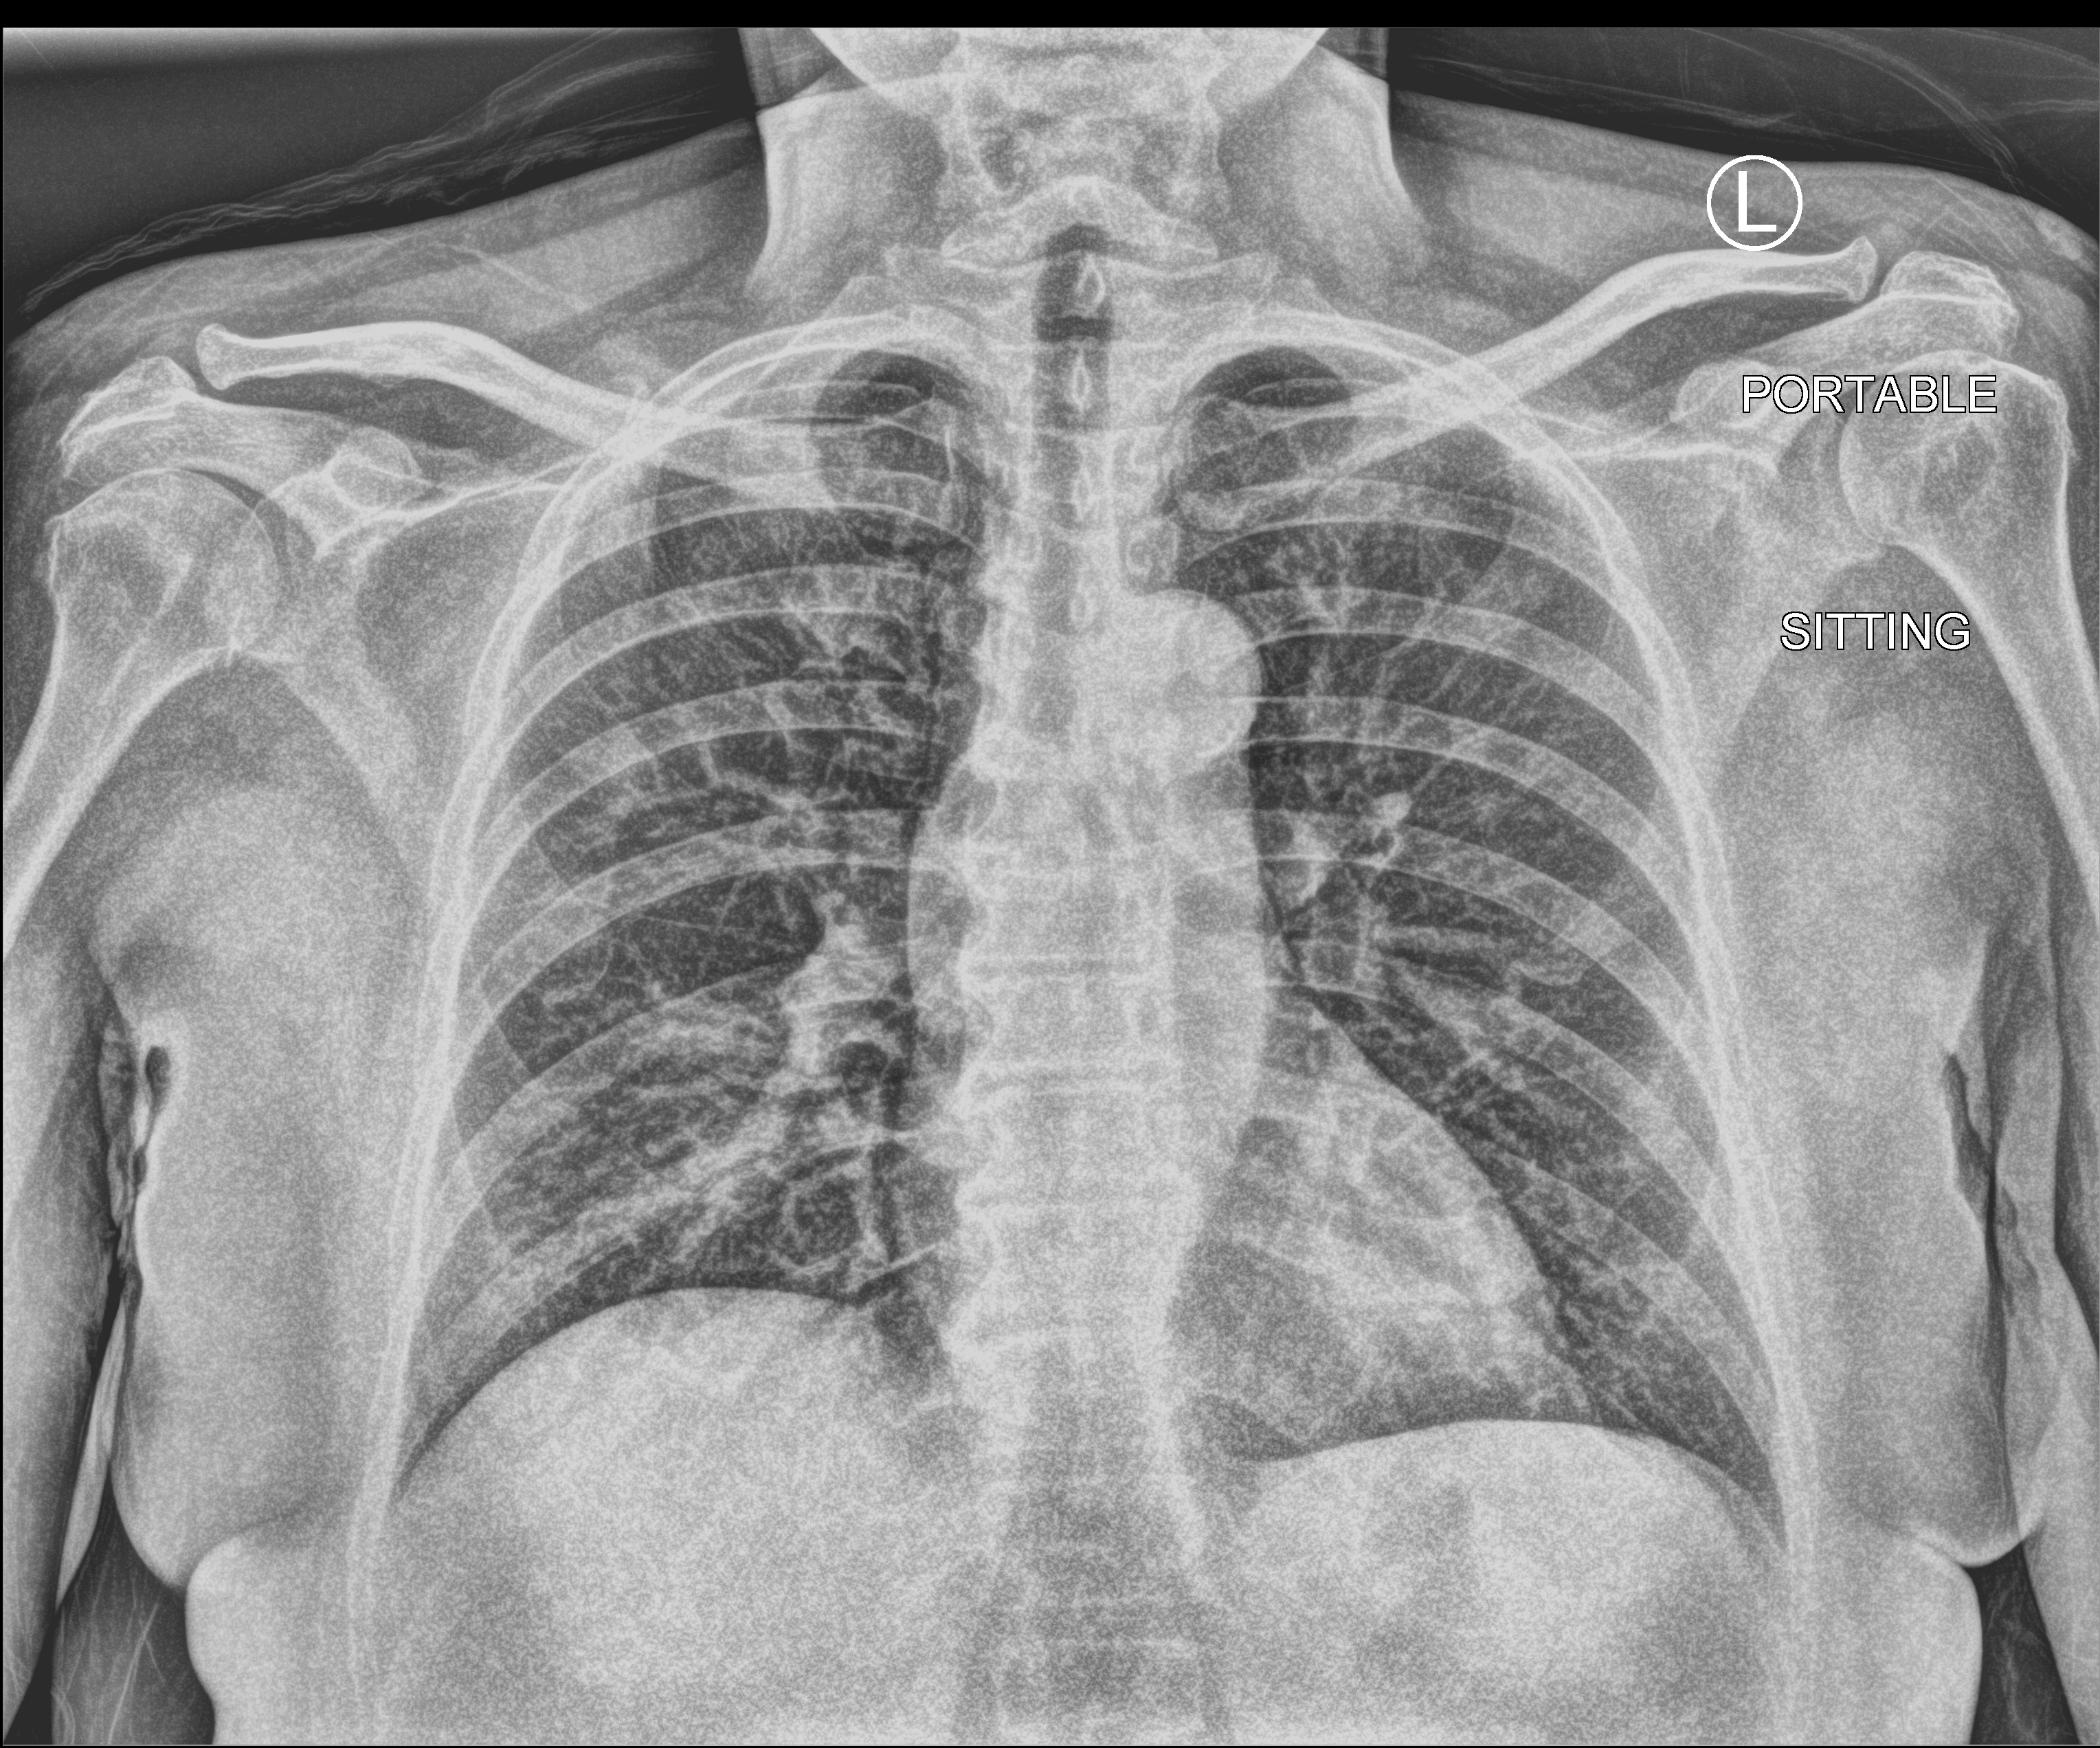
Chest X-ray (portable), anteroposterior (AP) projection. Female patient hospitalised with COVID-19, age 18–59 years.
Admission-level facts for this patient (not findings on this image; timing relative to this image not recorded): mechanically ventilated during this hospital stay: no; admitted to intensive care during this hospital stay: no.